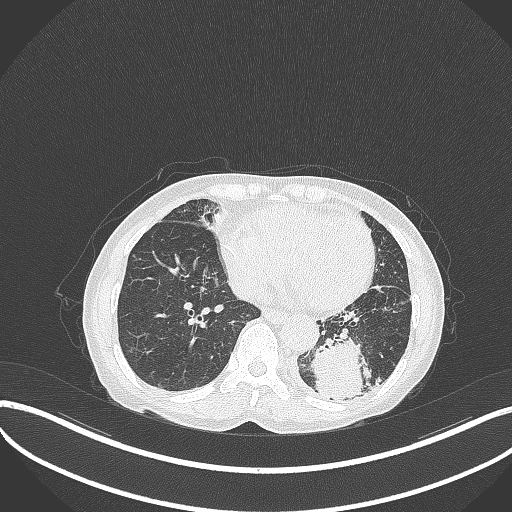
Chest CT, one axial slice; slice 96 of 370 in the series (ordered by position); 120 kVp; lung window (W 1500 / L -600 HU); 1 mm slice thickness; 512 × 512 image matrix, field of view 400 × 400 mm. Patient: female, 78 years. From the clinical record (not read from this slice): clinical TNM (as recorded): T3 N0 M1.
Structures marked on this image (bounding box drawn by a radiologist):
- lung tumour (recorded histology: squamous cell carcinoma): bounding box (x1, y1, x2, y2) in pixels: (308, 332, 371, 400)